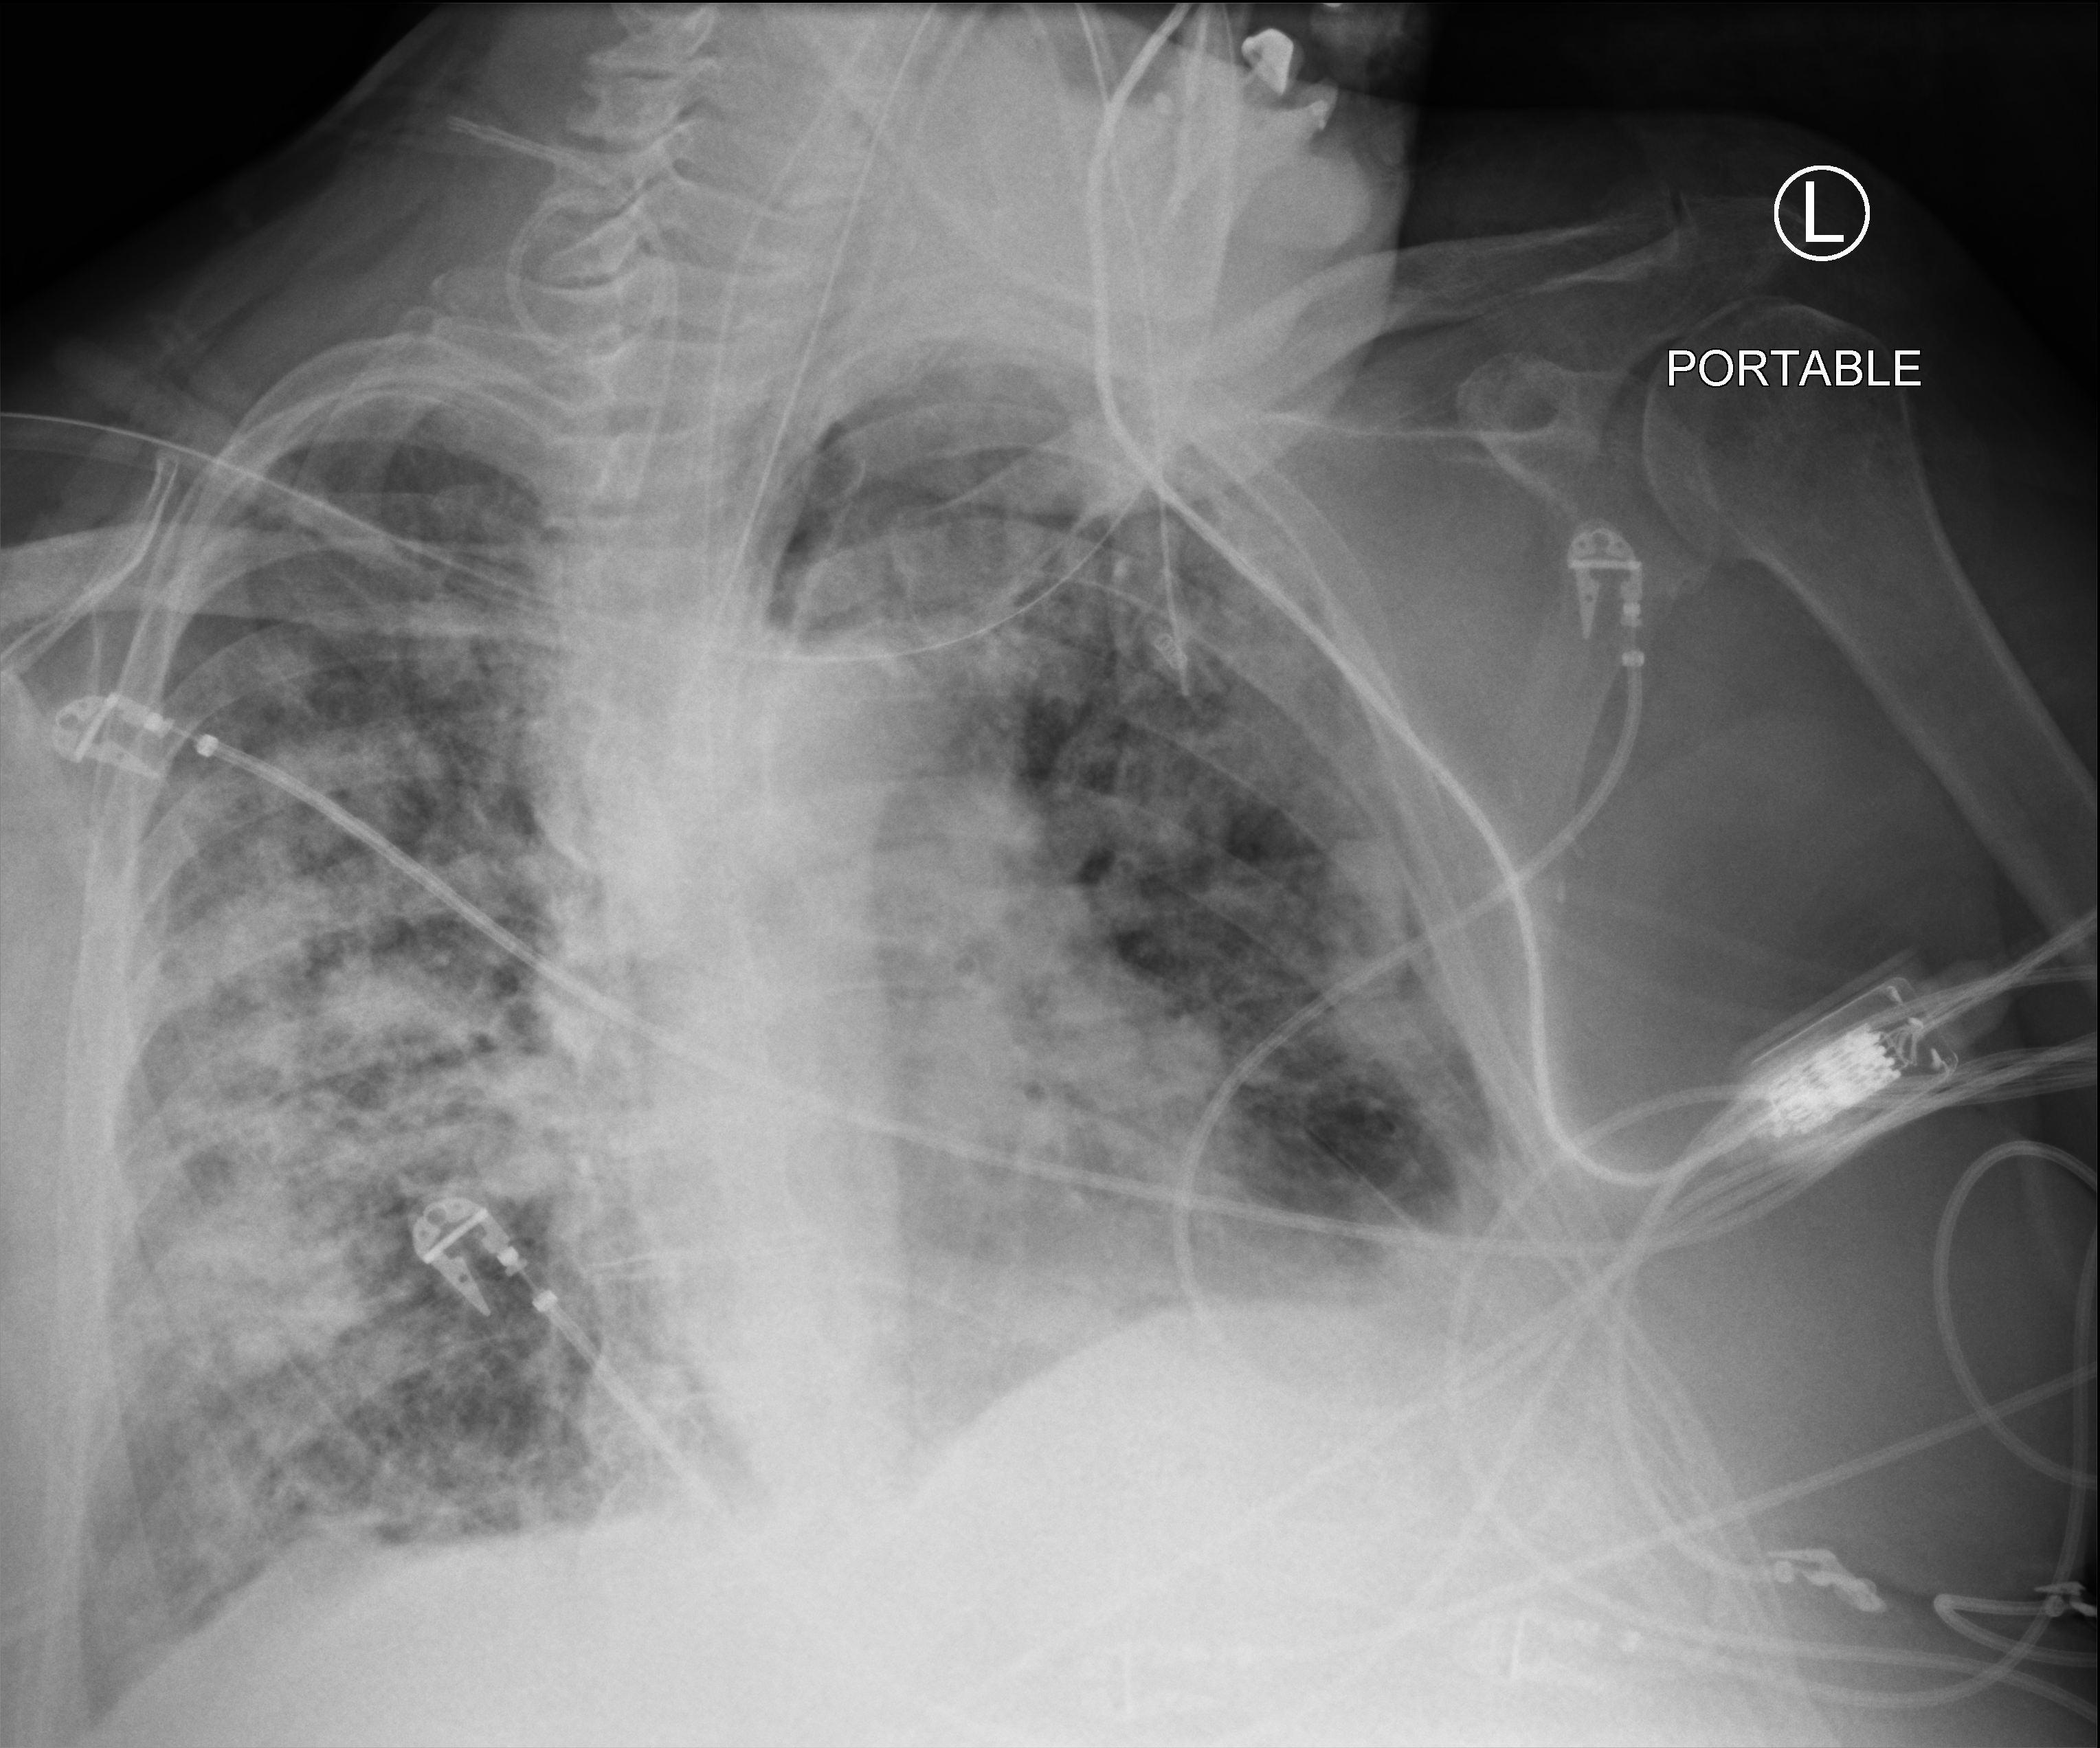
Portable chest radiograph, anteroposterior (AP) projection. Male patient hospitalised with COVID-19, age 60–74 years.
Hospital-stay facts (about this admission, not read from this image; timing relative to this image not recorded):
- diabetes (admission record): yes